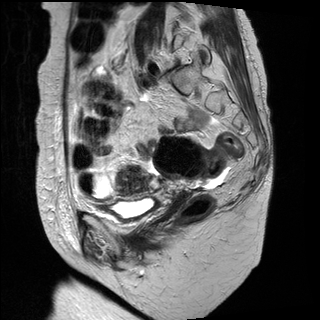
Pelvic MRI for cervical cancer, one sagittal slice; slice 20 of 31 in the series (ordered by position); T2-weighted; 1.5 T; TE 89 ms, TR 3890 ms; 4 mm slice thickness; 320 × 320 image matrix. Female patient, age 61 years.
Outlined on this slice (outlined manually by an expert reader):
- uterus and cervix: bounding box <115,165,152,195> (left, top, right, bottom; pixels)